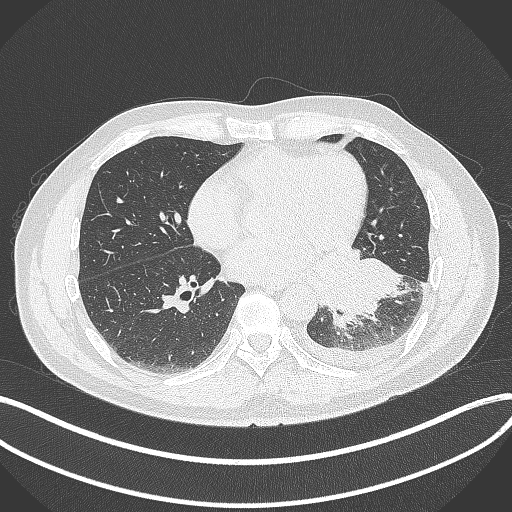
Chest CT, one axial slice. Reconstruction kernel B70f. 120 kVp. Lung window (W 1500 / L -600 HU). 512 × 512 image matrix, field of view 400 × 400 mm. Patient: male, 58 years. Case-level facts recorded for this patient, not image findings: clinical TNM (as recorded): T3 N1 M1b.
Structures marked on this image (rectangle marked by the reading radiologist):
- lung tumour (recorded histology: small cell carcinoma): bounding box [x1, y1, x2, y2] px = [316, 246, 408, 332]